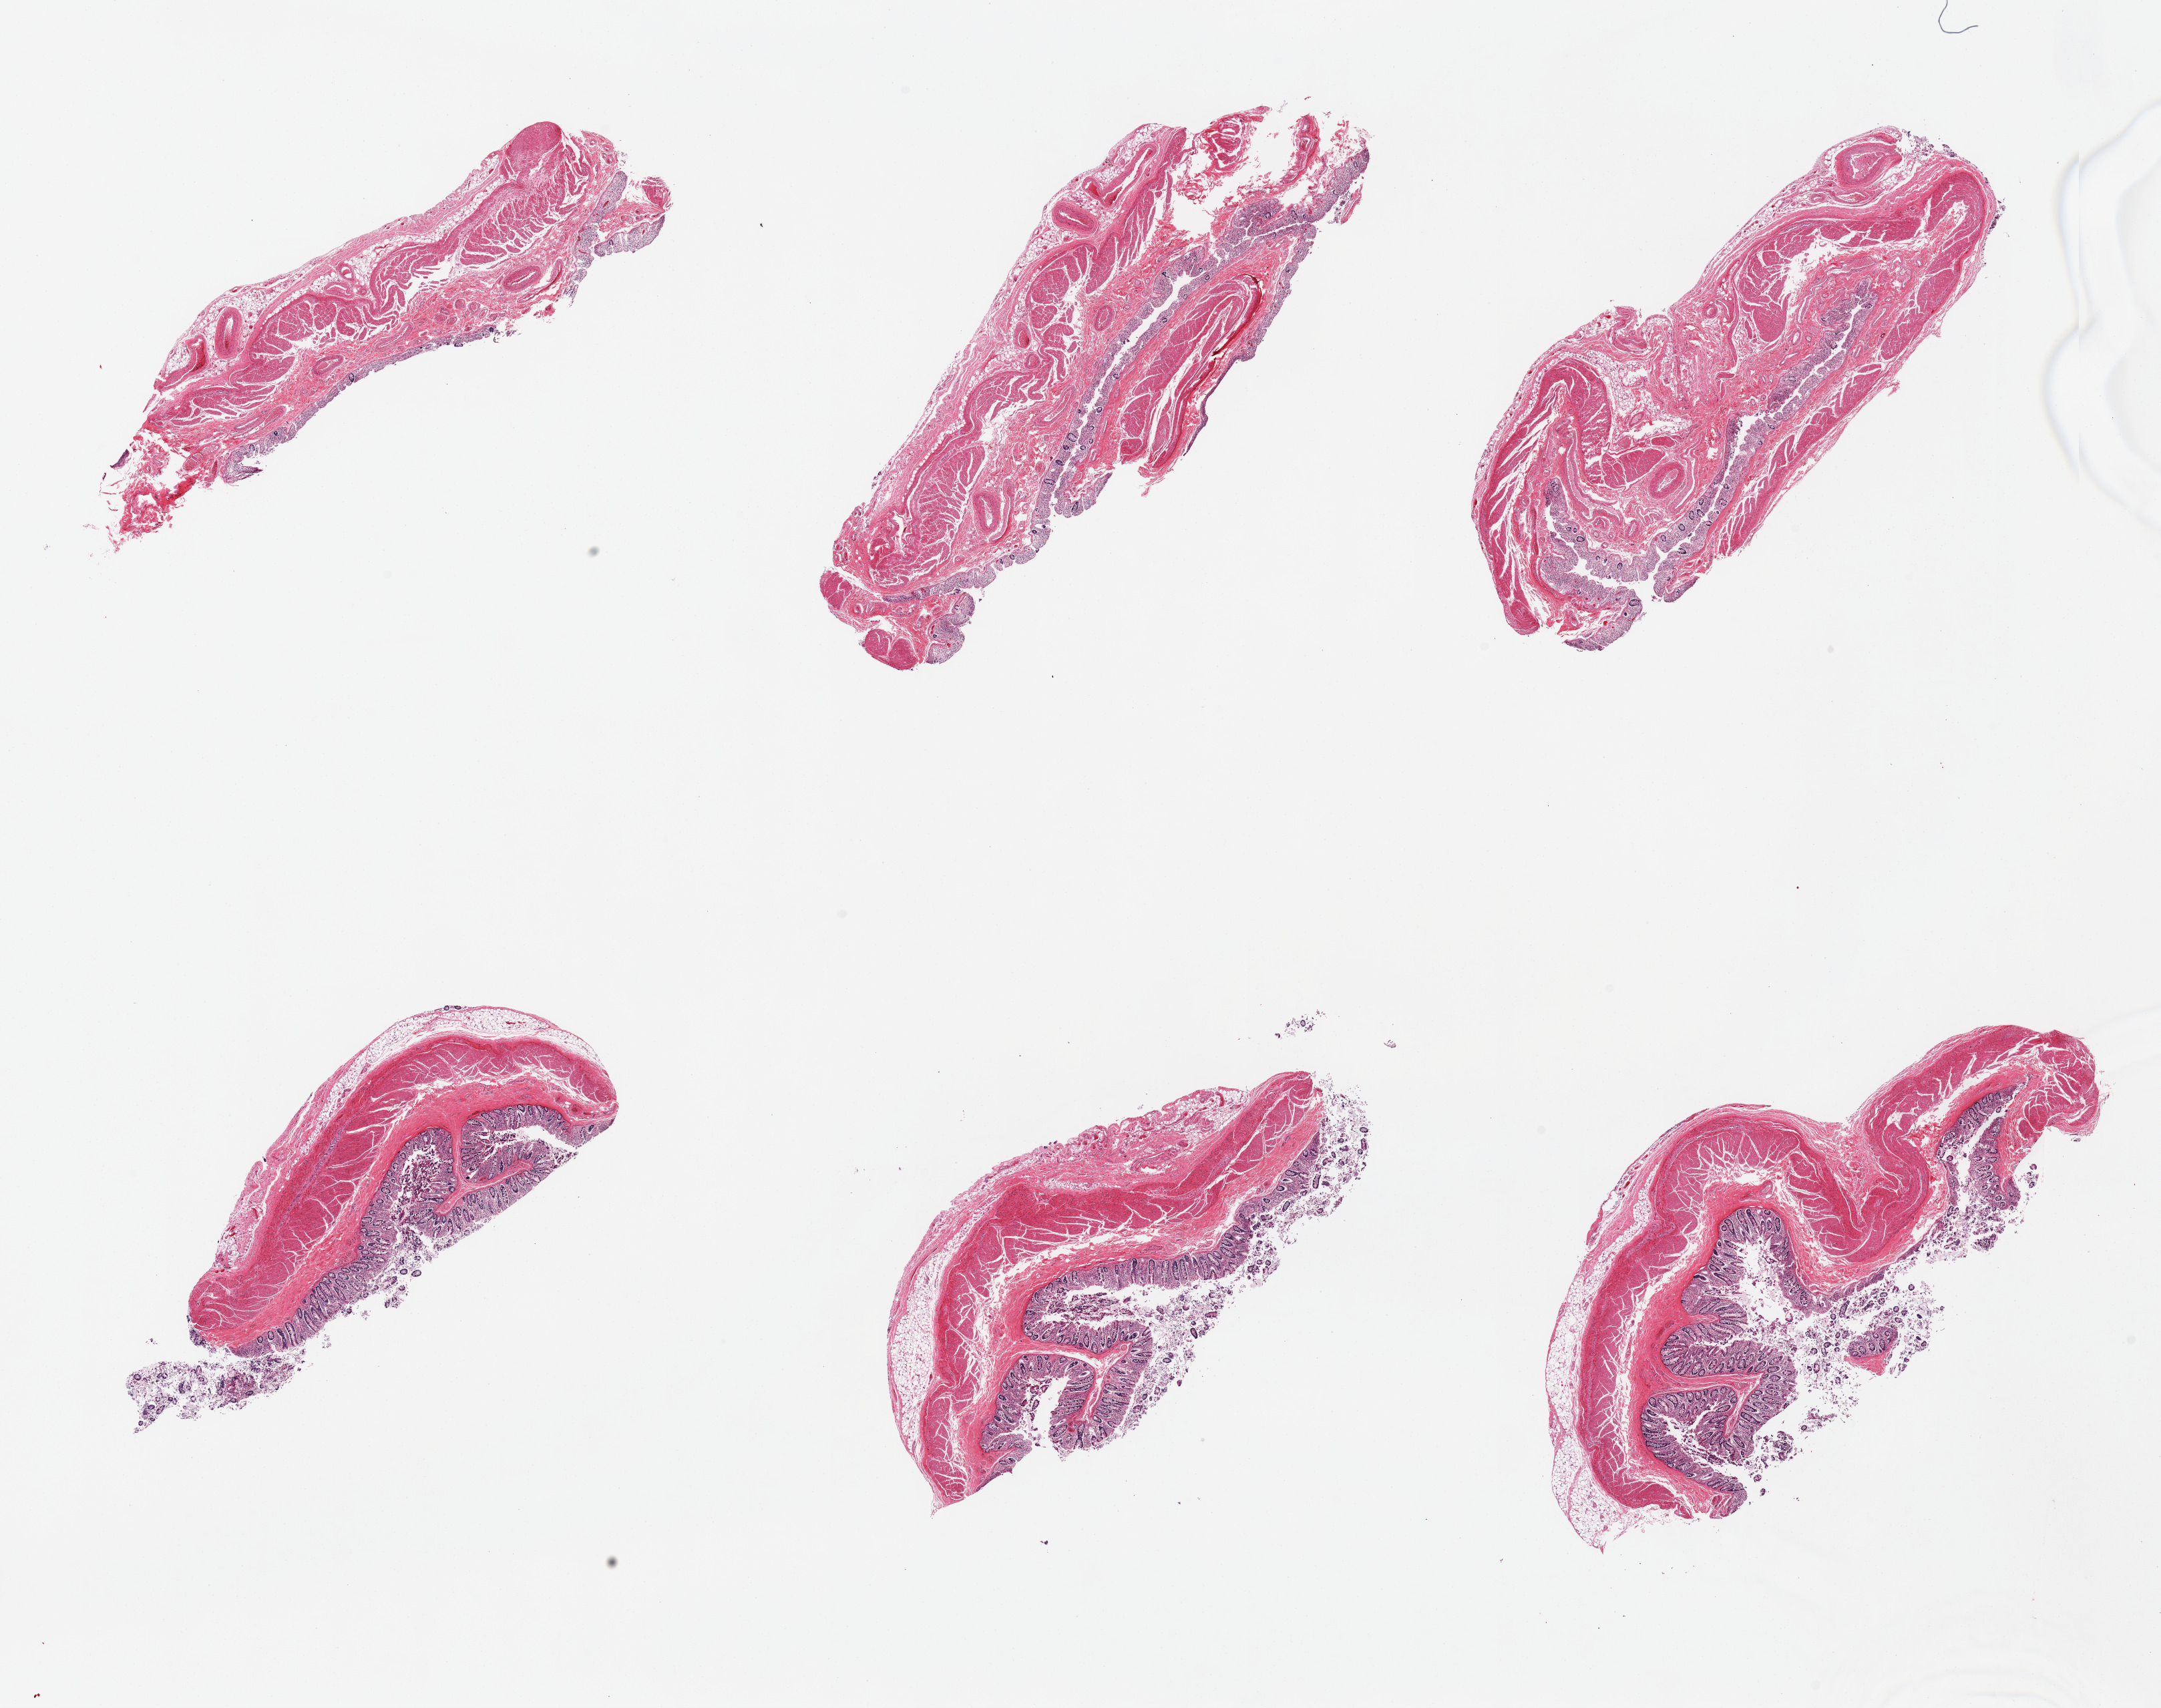
Whole-slide image, H&E stain — shown as a low-resolution overview of the whole scanned area (about 25.6 x 20.2 mm), PAXgene-fixed paraffin-embedded (PFPE) section, target tissue: transverse colon, tissue donor sample. Donor sex: male.
Reviewer comment on this tissue sample: 6 pieces; full thickness sections, variably autolyzed mucosa, thin rim of adherent fat.